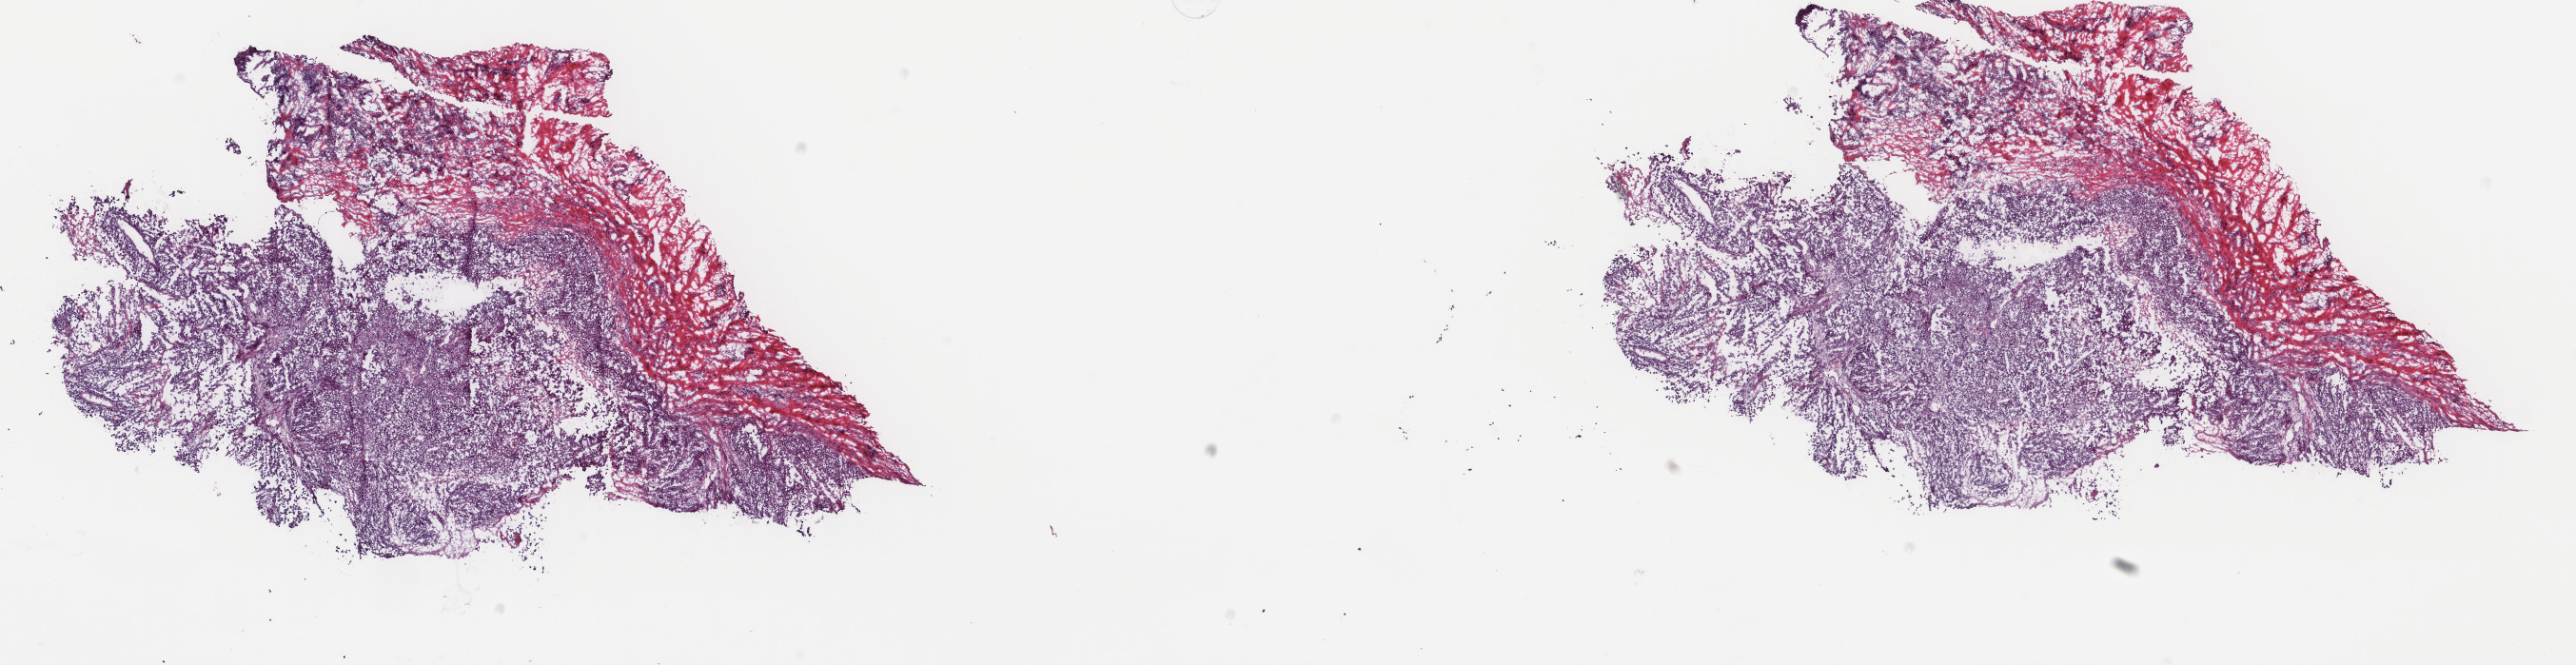
Digitized H&E-stained tissue section (whole slide) — a low-resolution overview of the entire scanned area, about 21.5 x 5.5 mm (from a 40x scan). Frozen section from the top of the tissue portion. Metastatic tumour sample. Patient: male, age at initial diagnosis 55 years. Composition of this section per pathologist review: tumour cells 75%, tumour nuclei 75%, normal cells 0%, stromal cells 25%, necrosis 0%. Inflammatory infiltration, as recorded: lymphocyte infiltration 5%, monocyte infiltration 0%, neutrophil infiltration 0%.
- this section: metastatic tumour tissue
- patient diagnosis: Malignant melanoma, NOS